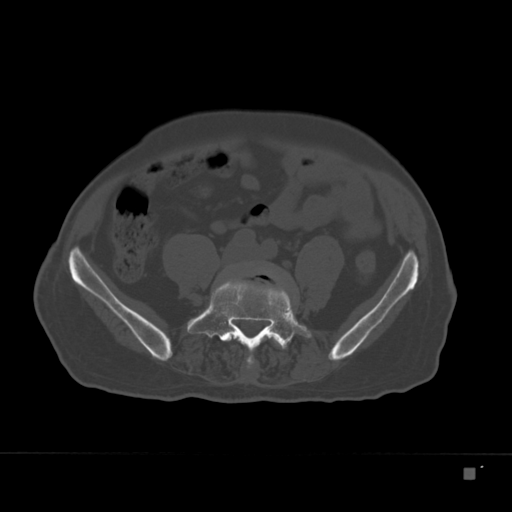
CT including the spine, one axial slice. Slice 28 of 332 in the series (ordered by position). Bone window (W 1800 / L 400 HU). 1.5 mm slice thickness. 512 × 512 image matrix, field of view 389 × 389 mm. Patient: male, 72 years. From the clinical record (not read from this slice): primary cancer: skeletal.
Annotated regions visible in this slice (semi-automatic segmentation, software-assisted and operator-edited):
- L4 vertebra: bounding box <246,268,281,368> (left, top, right, bottom; pixels)
- L5 vertebra: <192,280,311,355>